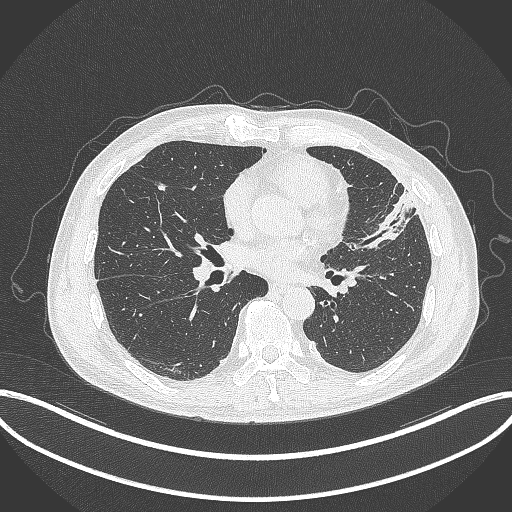
Chest CT, one axial slice. Slice 154 of 382 in the series (ordered by position). Reconstruction kernel B70f. Lung window (W 1500 / L -600 HU). 1 mm slice thickness. 512 × 512 image matrix, field of view 415 × 415 mm. Patient: male, 64 years. From the clinical record (not read from this slice): clinical TNM (as recorded): T4 N1 M0.
Outlined on this slice (bounding box drawn by a radiologist):
- lung tumour (recorded histology: adenocarcinoma): bounding box [x1, y1, x2, y2] px = [358, 184, 416, 247]